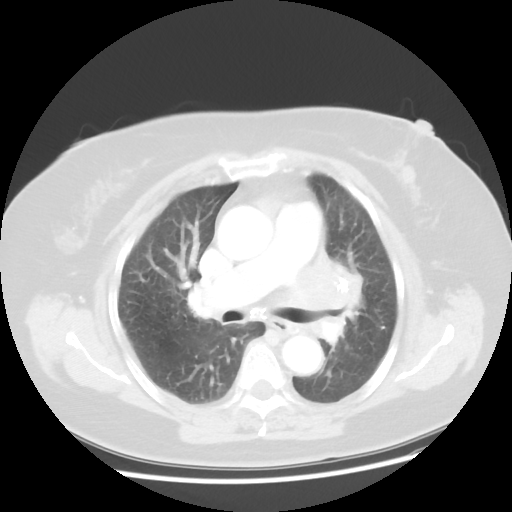
Chest CT, one axial slice. Slice 27 of 49 in the series (ordered by position). Lung window (W 1500 / L -600 HU). 512 × 512 image matrix, field of view 374 × 374 mm. Female patient, age 58 years. Case-level facts recorded for this patient, not image findings: clinical TNM (as recorded): T4 N3 M0.
Annotated regions visible in this slice (bounding box drawn by a radiologist):
- lung tumour (recorded histology: small cell carcinoma): box from (x=286, y=252) to (x=363, y=347) px